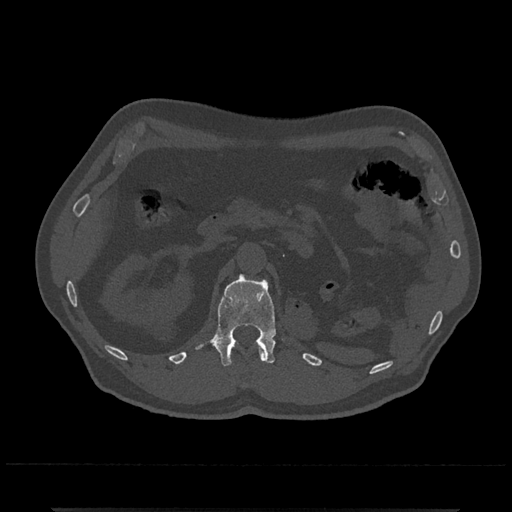
CT including the spine, one axial slice. Slice 375 of 797 in the series (ordered by position). Reconstruction kernel Br40s/3. 120 kVp. Bone window (W 1800 / L 400 HU). 0.5 mm slice thickness. 512 × 512 image matrix, field of view 393 × 393 mm. Male patient, age 67 years. Case-level facts recorded for this patient, not image findings: primary cancer: prostate.
Outlined on this slice (semi-automatically segmented with operator editing):
- L1 vertebra: bounding box [x1, y1, x2, y2] px = [195, 273, 276, 366]
- T12 vertebra: [259, 346, 267, 361]